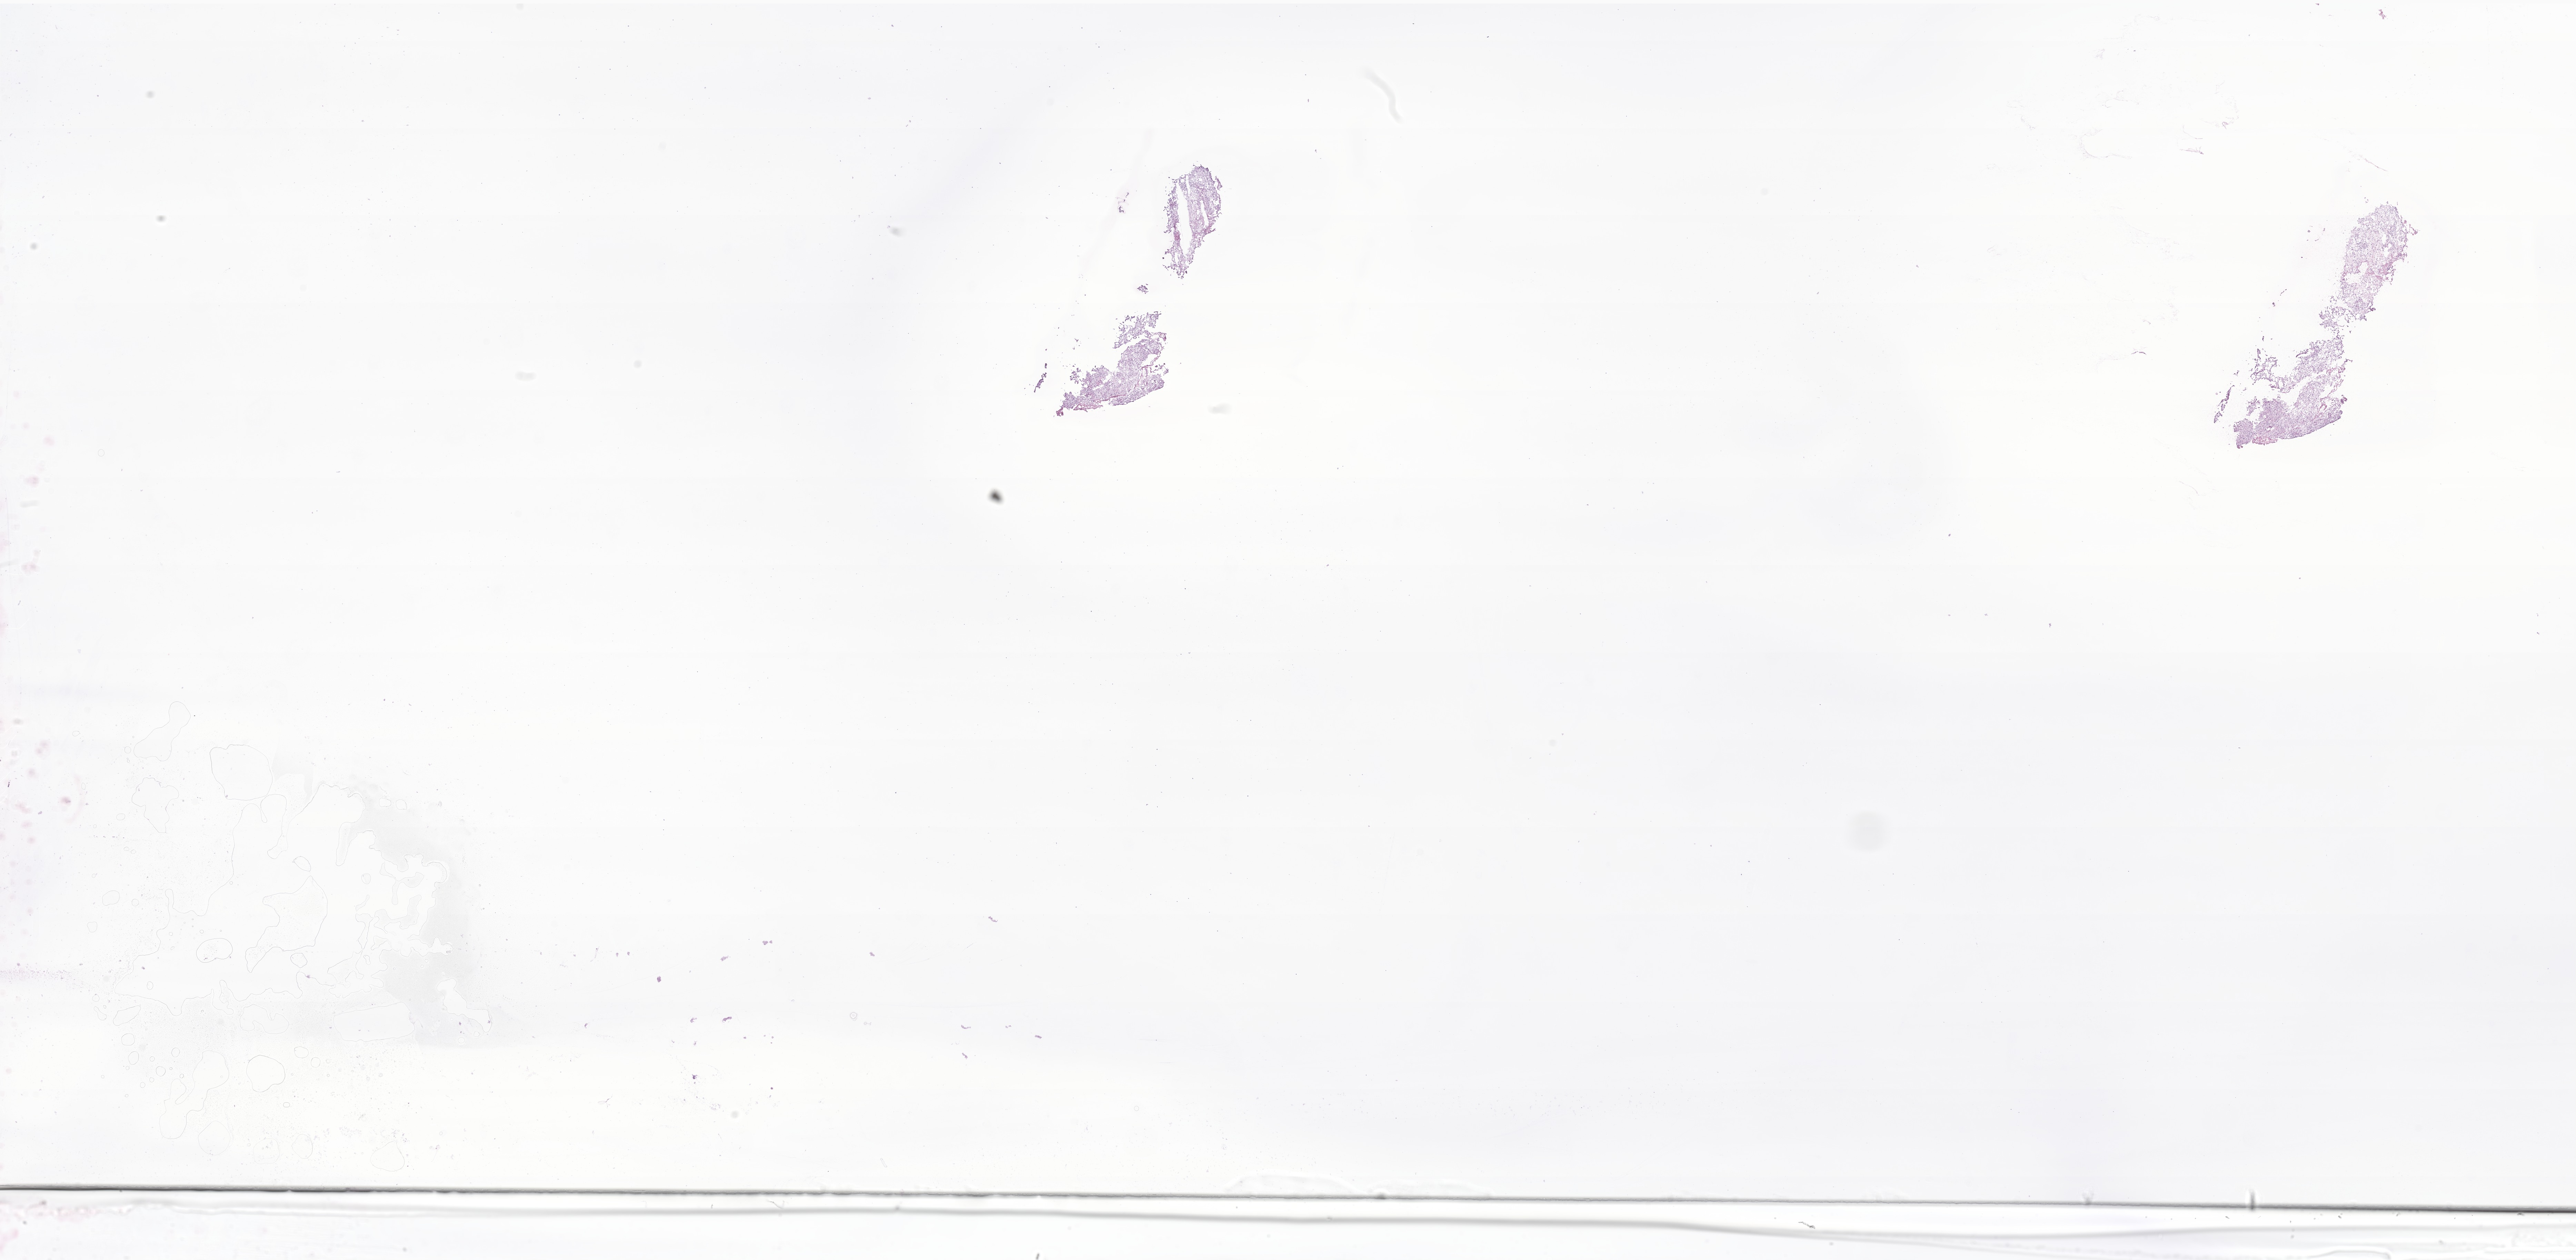
Digitized hematoxylin and eosin (H&E)-stained section of tumor tissue from the brain, low-resolution overview of the scanned area, about 31.5 x 15.4 mm. Frozen section. Male patient, age 921 days (about 2.5 years).
• recorded diagnosis: Pilocytic astrocytoma